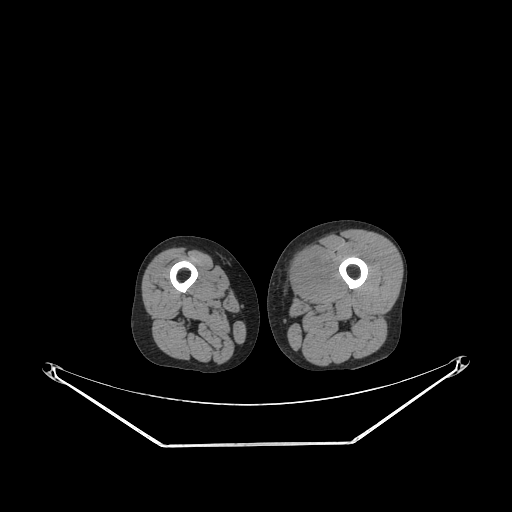
CT of an extremity soft-tissue mass (from a PET/CT study), one axial slice. Position 221 of 267 along the scan axis. Reconstruction kernel STANDARD. 140 kVp. Soft-tissue window (W 400 / L 40 HU). 3.75 mm slice thickness. 512 × 512 image matrix. Male patient. From the clinical record (not read from this slice): histological type: pleiomorphic leiomyosarcoma; grade: high; site of the primary tumour: left thigh.
Structures marked on this image (expert contour drawn on MRI and transferred to this co-registered scan by the dataset authors):
- gross tumour volume including surrounding oedema: bounding box (x1, y1, x2, y2) in pixels: (285, 249, 330, 298)
- gross tumour volume (mass): (285, 249, 327, 298)